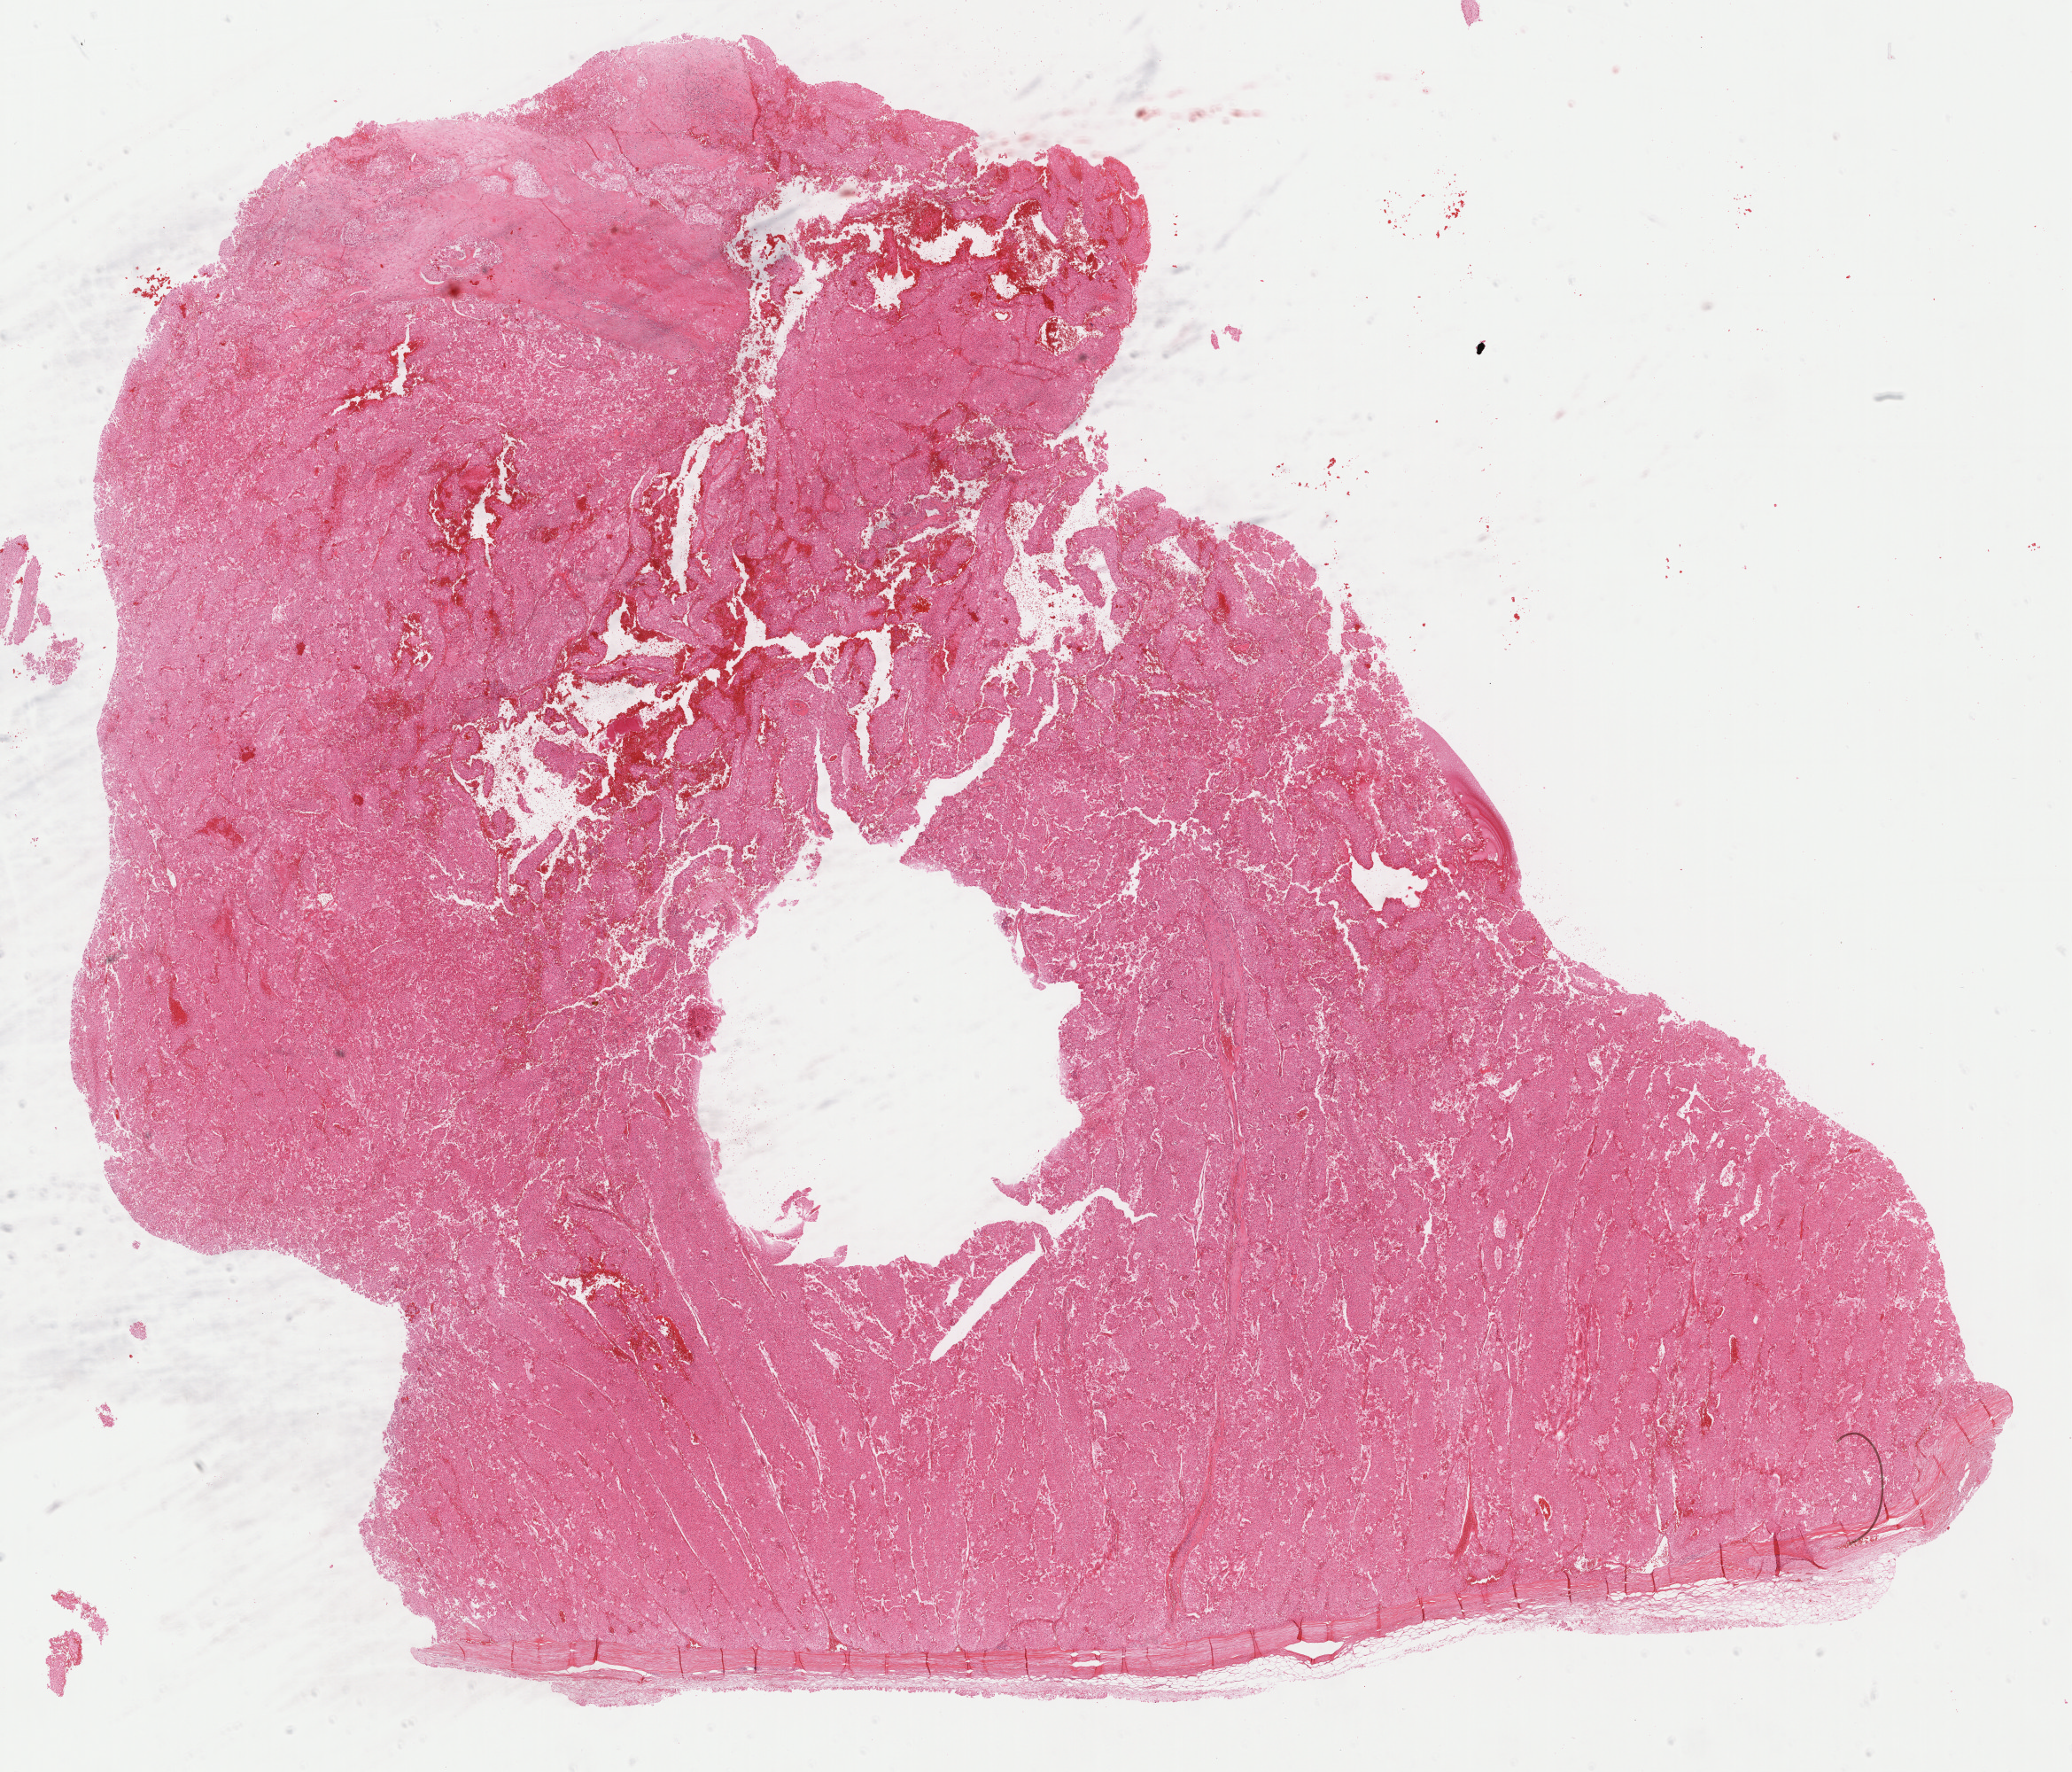
Digitized H&E-stained tissue section (whole slide), low-resolution overview of the scanned area, about 18.9 x 16.1 mm (from a 40x scan); FFPE section; kidney, primary tumour sample. Patient: male, age at initial diagnosis 59 years.
• pathologic diagnosis: Renal cell carcinoma, chromophobe type
• AJCC pathologic stage: II (6th edition)